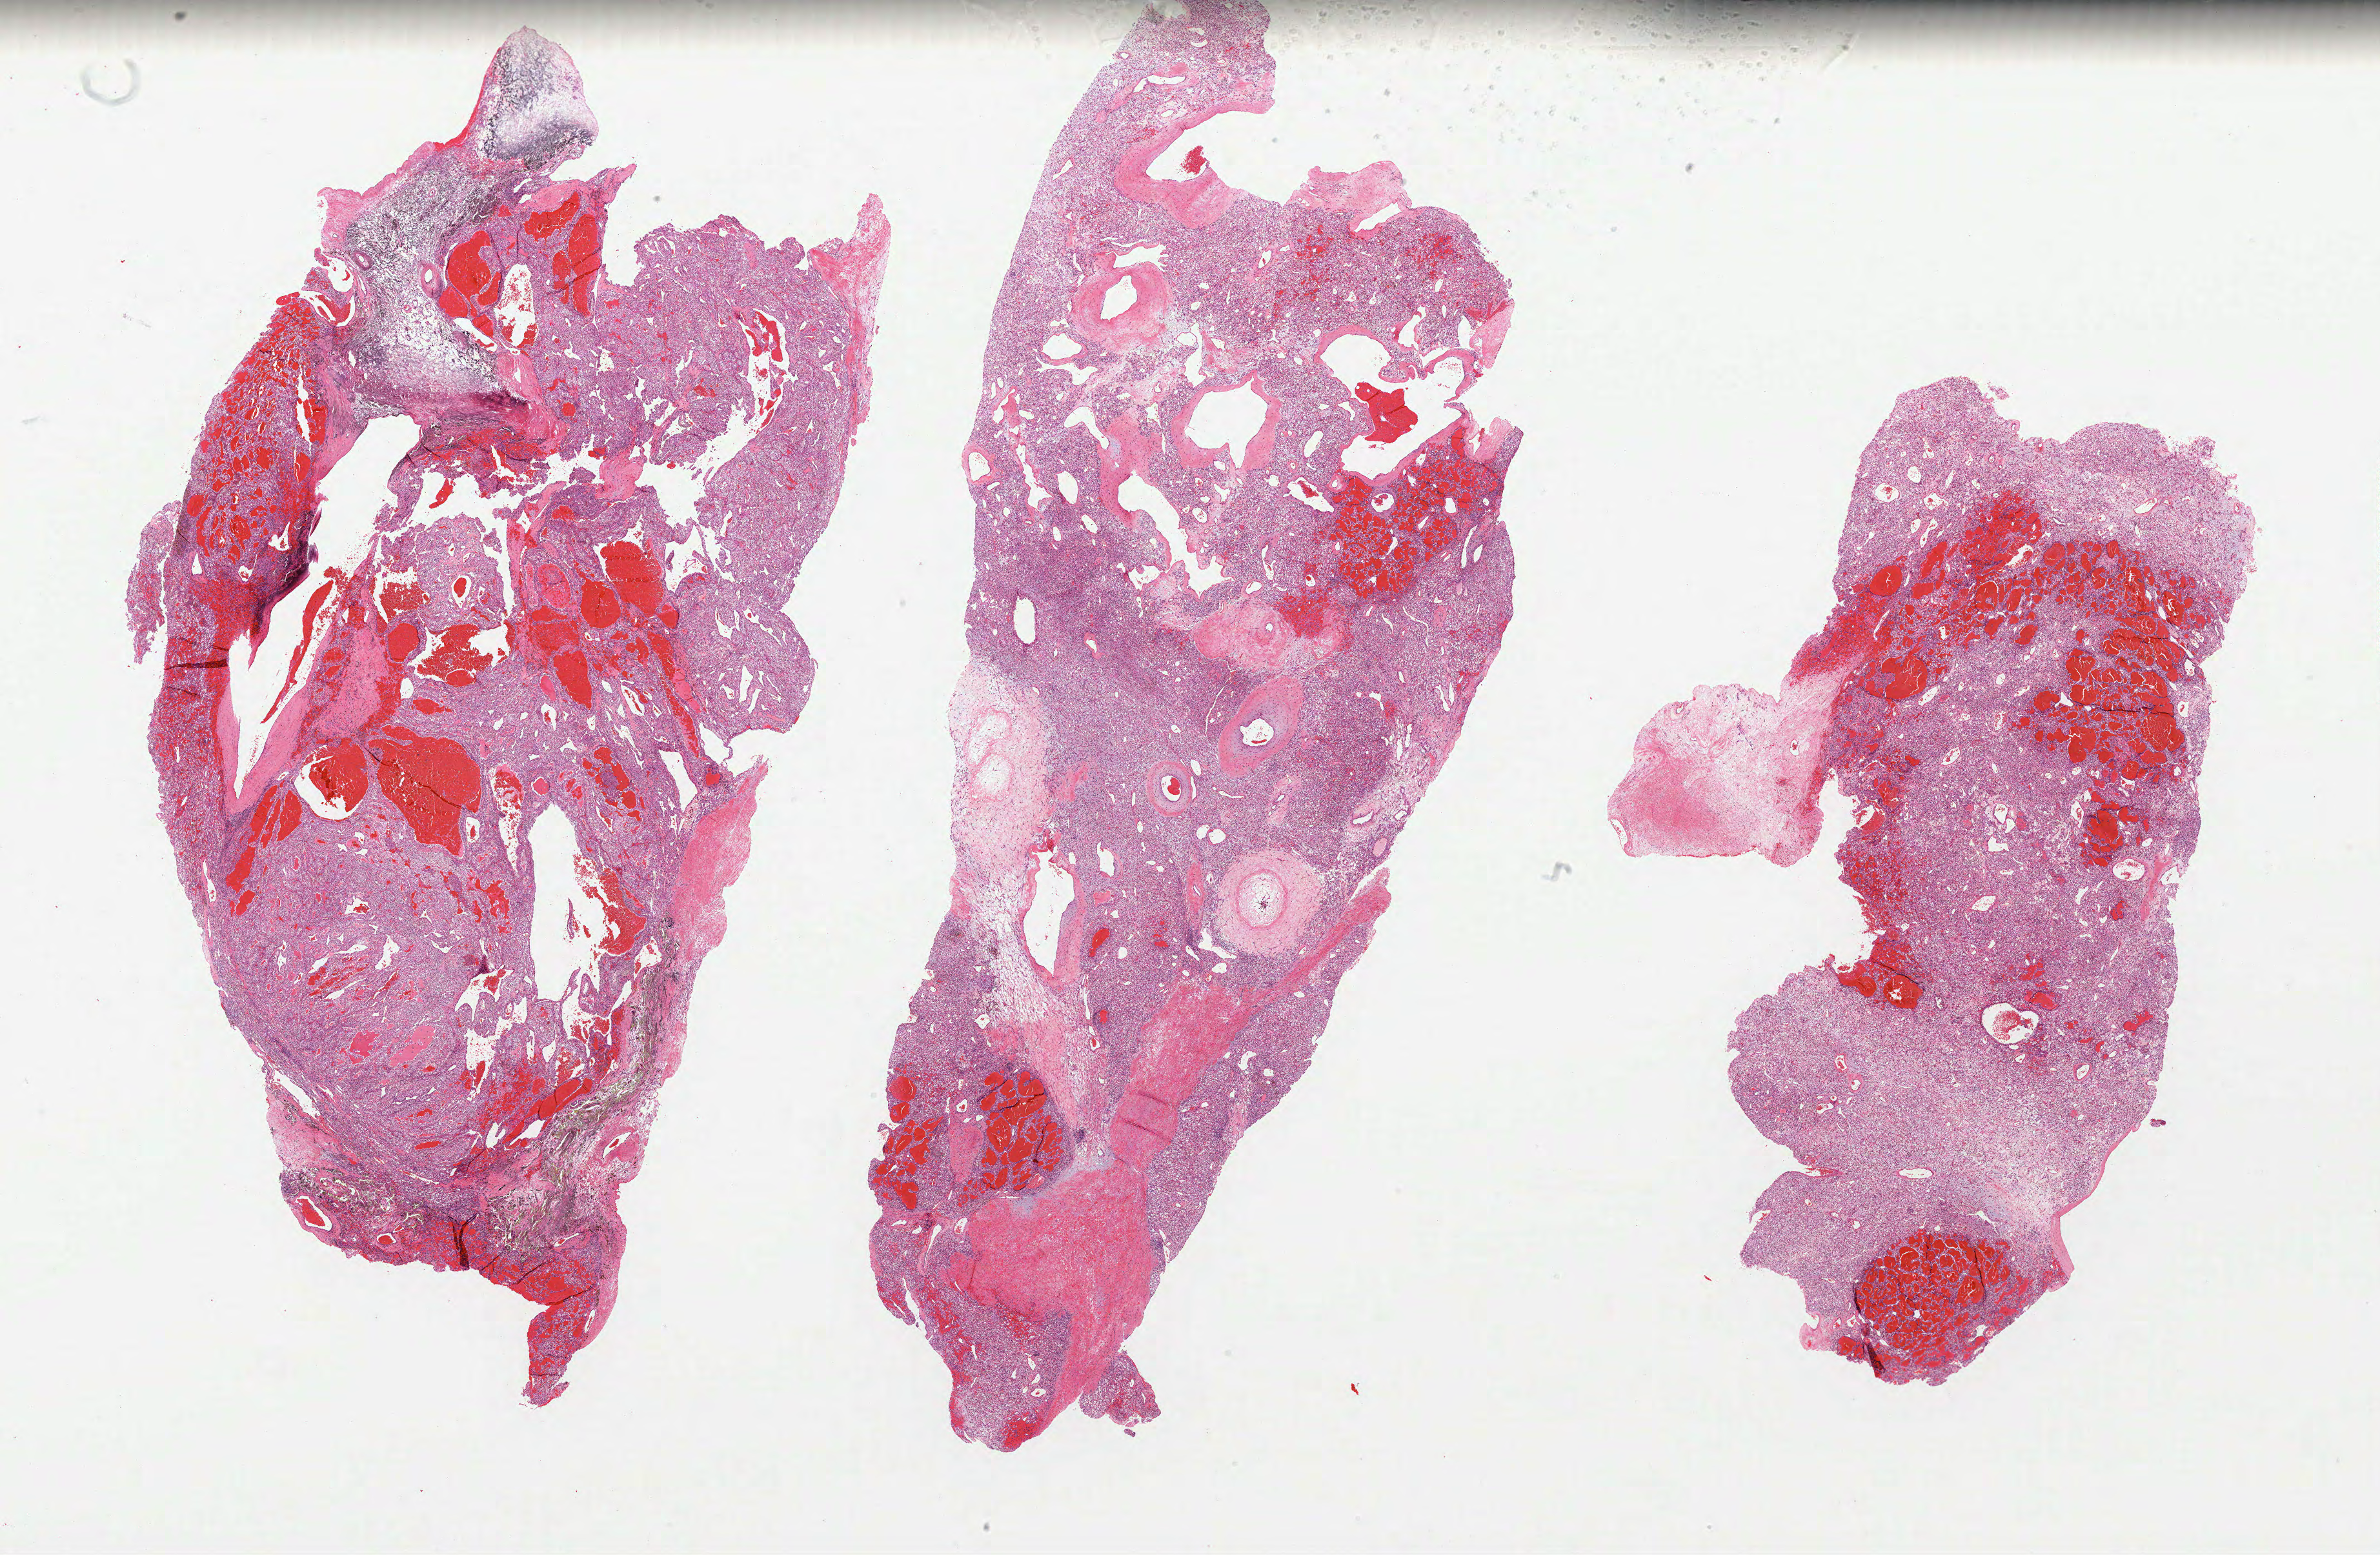
Whole-slide histology image, H&E-stained — a low-resolution overview of the entire scanned area, about 29.7 x 19.4 mm (from a 40x scan), formalin-fixed paraffin-embedded (FFPE) diagnostic section, primary tumour sample from the kidney. Patient: male, age at initial diagnosis 76 years.
Histologic diagnosis: Clear cell adenocarcinoma, NOS.